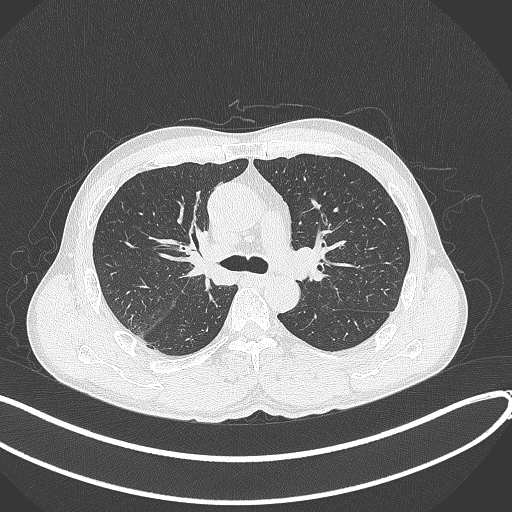
Chest CT, one axial slice; position 247 of 409 along the scan axis; reconstruction kernel B70f; 120 kVp; lung window (W 1500 / L -600 HU); 1 mm slice thickness; 512 × 512 image matrix, field of view 400 × 400 mm. Patient: male, 53 years. From the clinical record (not read from this slice): clinical TNM (as recorded): T1b N0 M0.
Outlined on this slice (rectangle marked by the reading radiologist):
- lung tumour (recorded histology: squamous cell carcinoma): box from (x=174, y=223) to (x=234, y=291) px